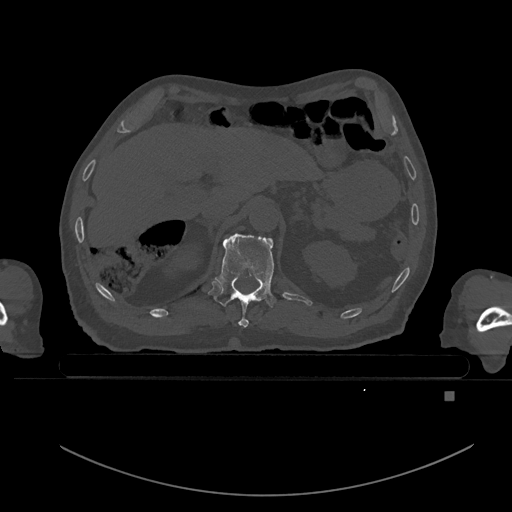
CT including the spine, one axial slice; position 29 of 969 along the scan axis; bone window (W 1800 / L 400 HU); 0.5 mm slice thickness; 512 × 512 image matrix. Patient: male, 82 years. From the clinical record (not read from this slice): primary cancer: prostate; vertebrae with lytic lesions (as recorded): T11, T9, T8, T2.
Structures marked on this image (semi-automatic segmentation, software-assisted and operator-edited):
- T11 vertebra: box from (x=215, y=233) to (x=278, y=327) px